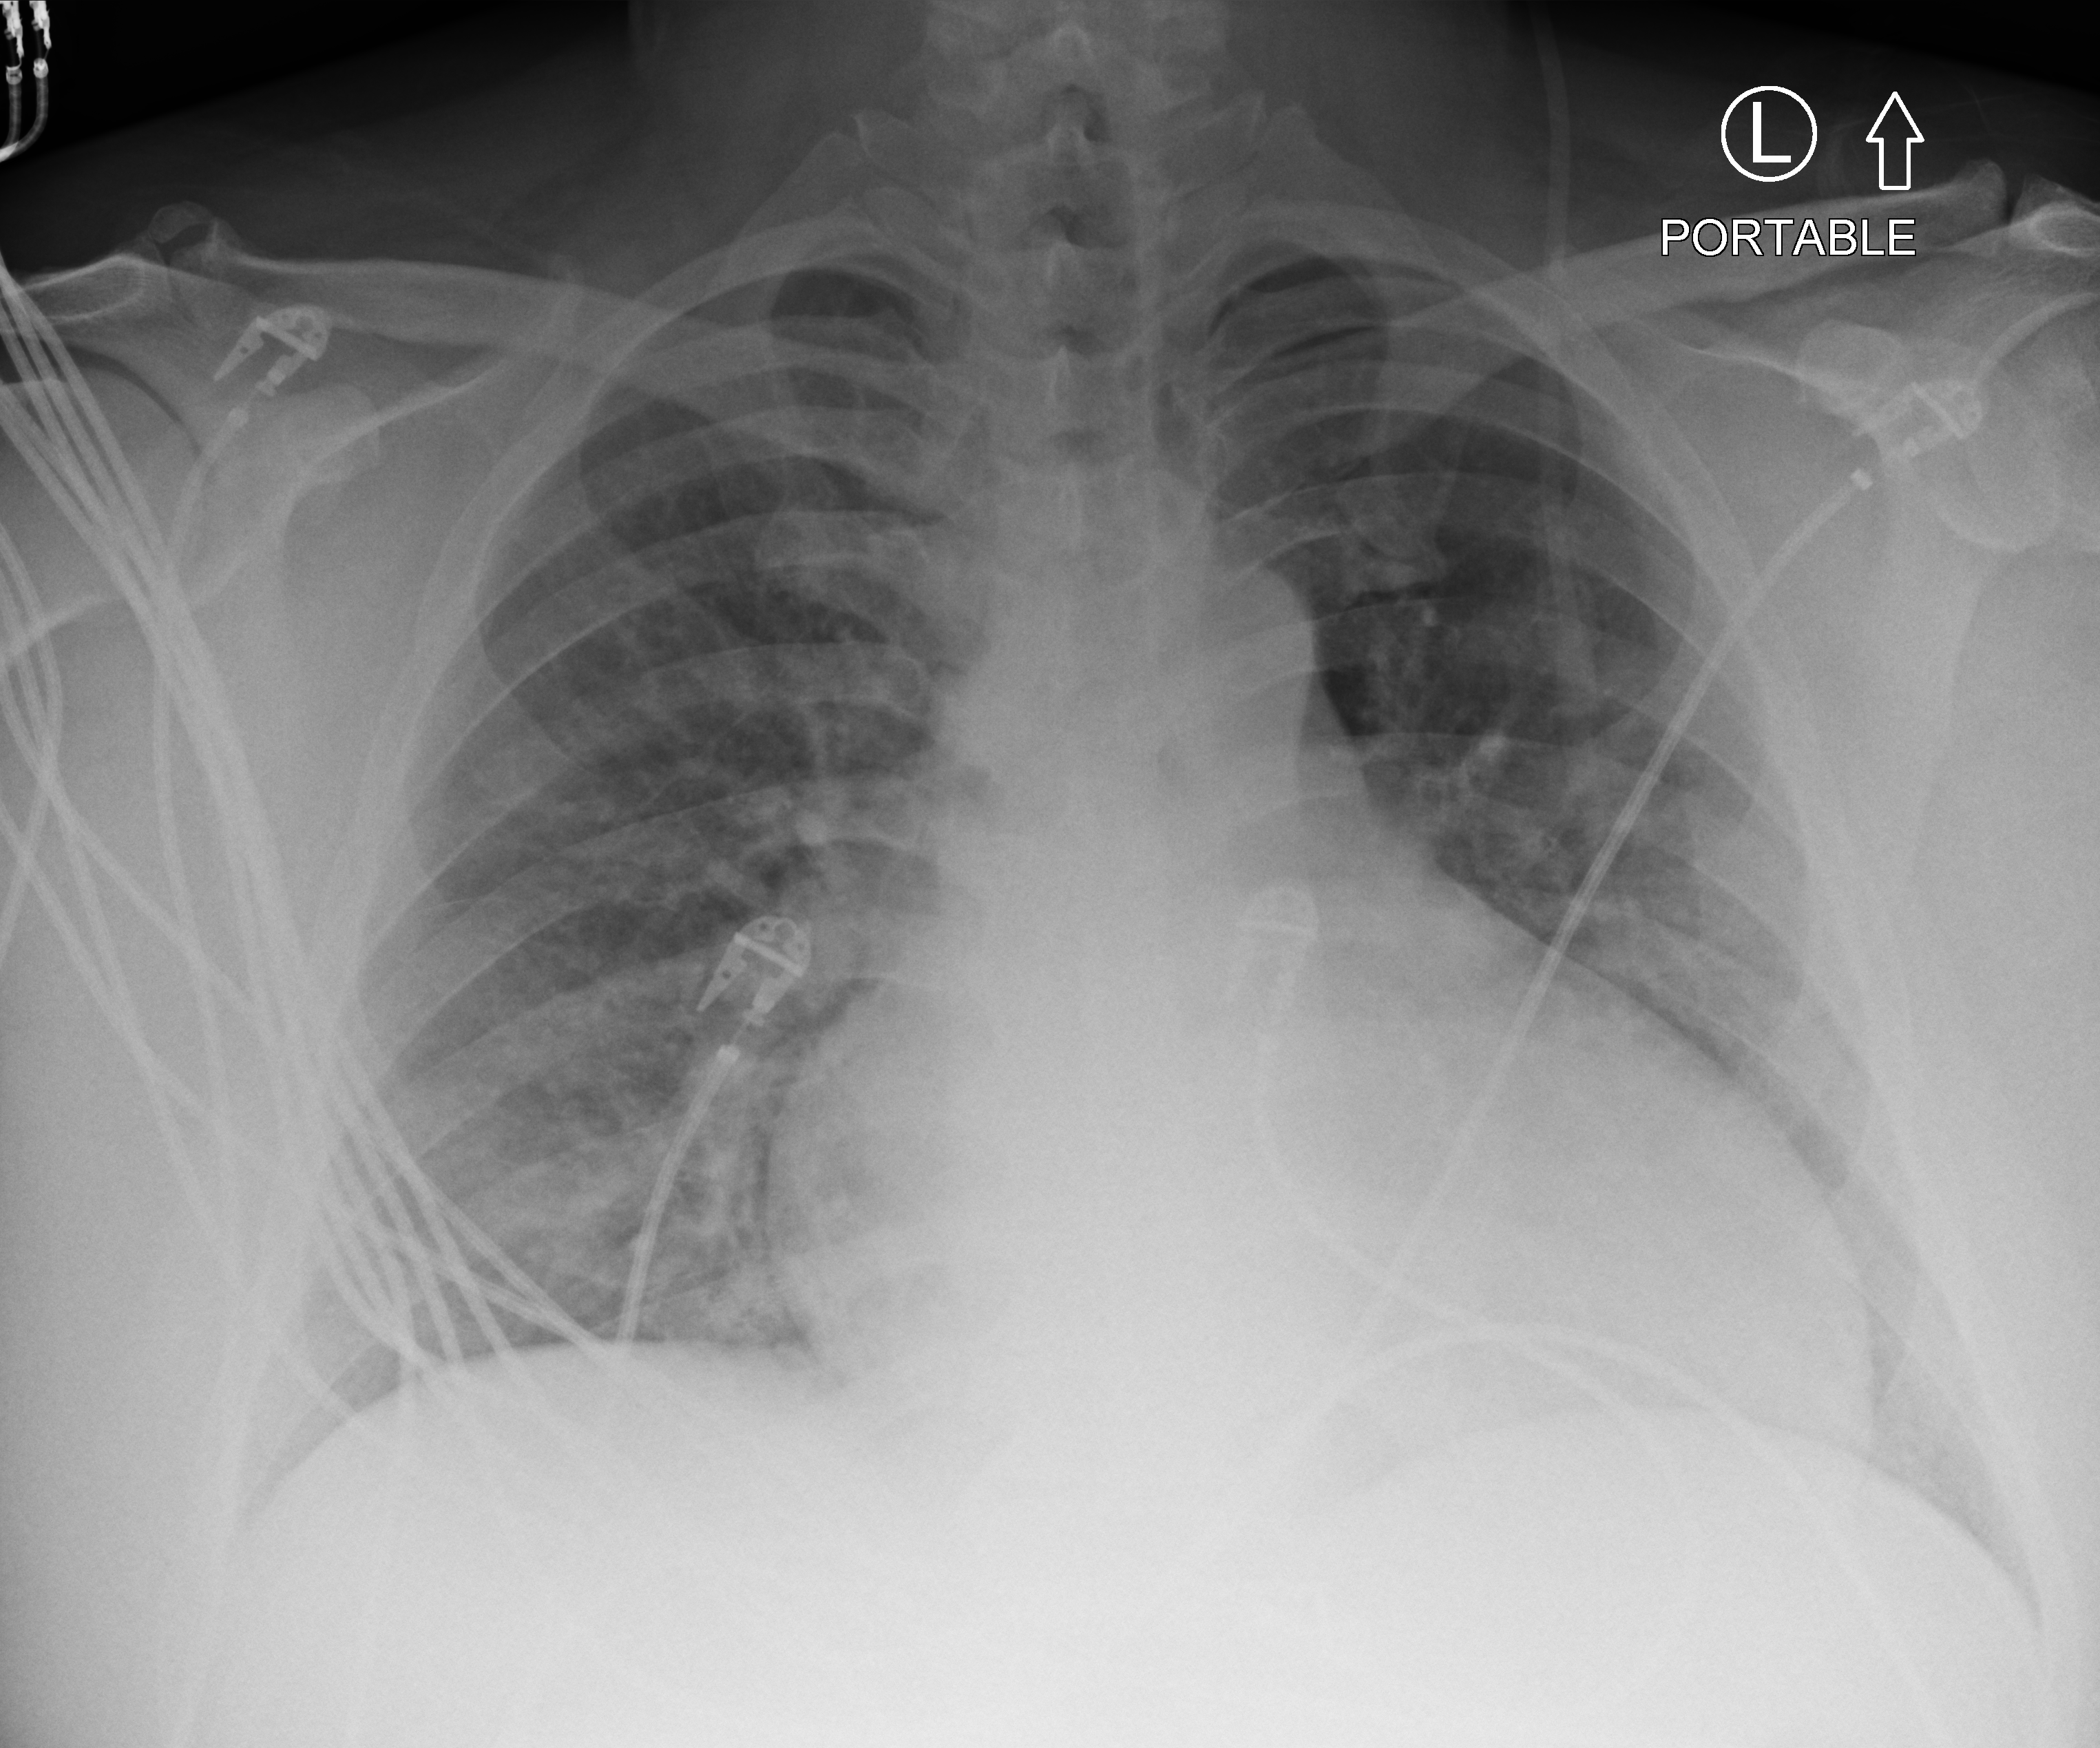
Bedside chest radiograph (computed radiography). Male patient hospitalised with COVID-19, age 18–59 years.
Hospital-stay facts (about this admission, not read from this image; timing relative to this image not recorded): admitted to intensive care during this hospital stay: no; smoking status (admission record): current; mechanically ventilated during this hospital stay: no.